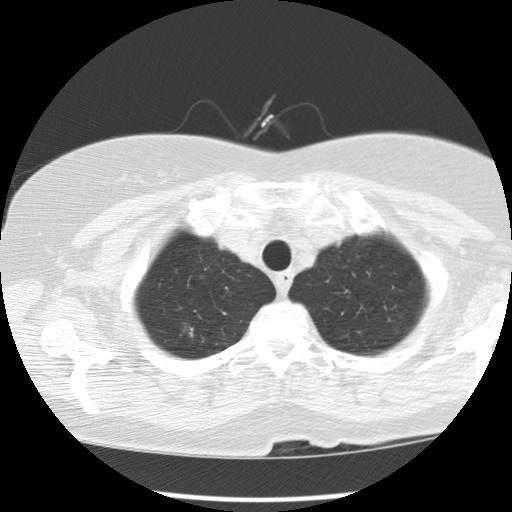
Chest CT (low-dose screening protocol), one axial image. Third screening round (two years after baseline). Lung window (W 1500 / L -600 HU). 2.5 mm slice thickness. 120 kVp. Female, age 72 years at enrolment. Former smoker at enrolment.
Lesion marked by an expert reader, bounding box <165,314,208,352> (left, top, right, bottom; pixels). The screening reader recorded 4 non-calcified nodules or masses ≥4 mm on this exam (right upper lobe, right upper lobe, right upper lobe, right lower lobe); which of them this box marks is not recorded. Participant outcome: lung cancer diagnosed 85 days after this screen — bronchiolo-alveolar adenocarcinoma, NOS, right upper lobe, well differentiated (G1), stage IA (AJCC 6th edition), 8 mm at pathology.